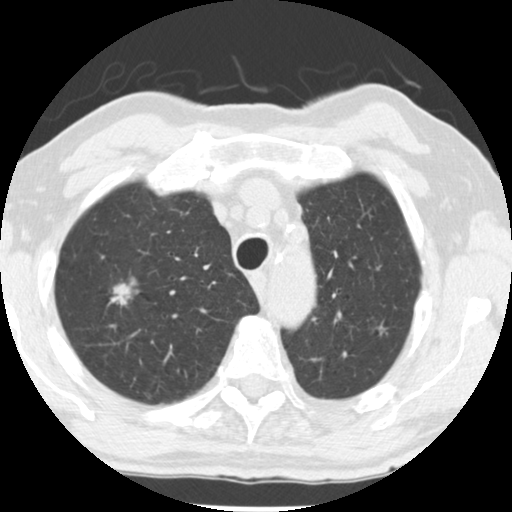
Chest CT (low-dose screening protocol), one axial image; baseline annual screen; lung window (W 1500 / L -600 HU); 2.5 mm slice thickness; standard (soft-tissue) reconstruction kernel (STANDARD); slice 201 of 252 in the series; 512 × 512 image matrix, field of view 313 × 313 mm. Male participant, aged 69 years at enrolment.
Lesion marked by an expert reader, box from (x=92, y=269) to (x=152, y=325) px. The screening reader recorded 2 non-calcified nodules or masses ≥4 mm on this exam (right upper lobe, left upper lobe); which of them this box marks is not recorded. Official screen result: positive, change unspecified: nodule(s) >= 4 mm or enlarging nodule(s), mass(es), or other non-specific abnormalities suspicious for lung cancer. Participant outcome: lung cancer diagnosed 105 days after this screen — adenocarcinoma, NOS, right upper lobe, well differentiated (G1), stage IA (AJCC 6th edition), 17 mm at pathology.